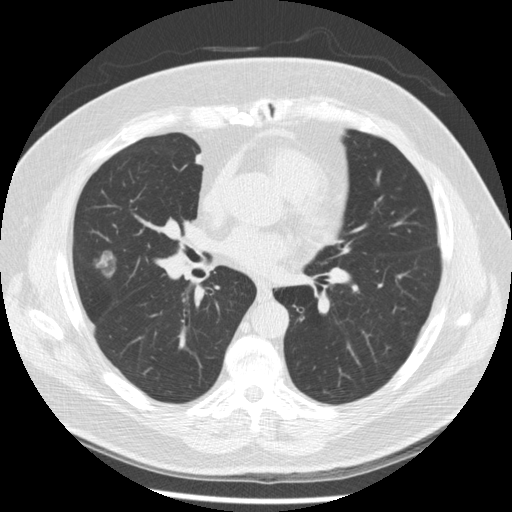
Low-dose screening chest CT, one axial slice; slice 115 of 230 in the series (ordered by position); 120 kVp; lung window (W 1500 / L -600 HU); 2.5 mm slice thickness; 512 × 512 image matrix.
Outlined on this slice (outlined manually by an expert reader):
- lesion 1 (tumor, middle lobe of right lung): box from (x=96, y=250) to (x=115, y=277) px